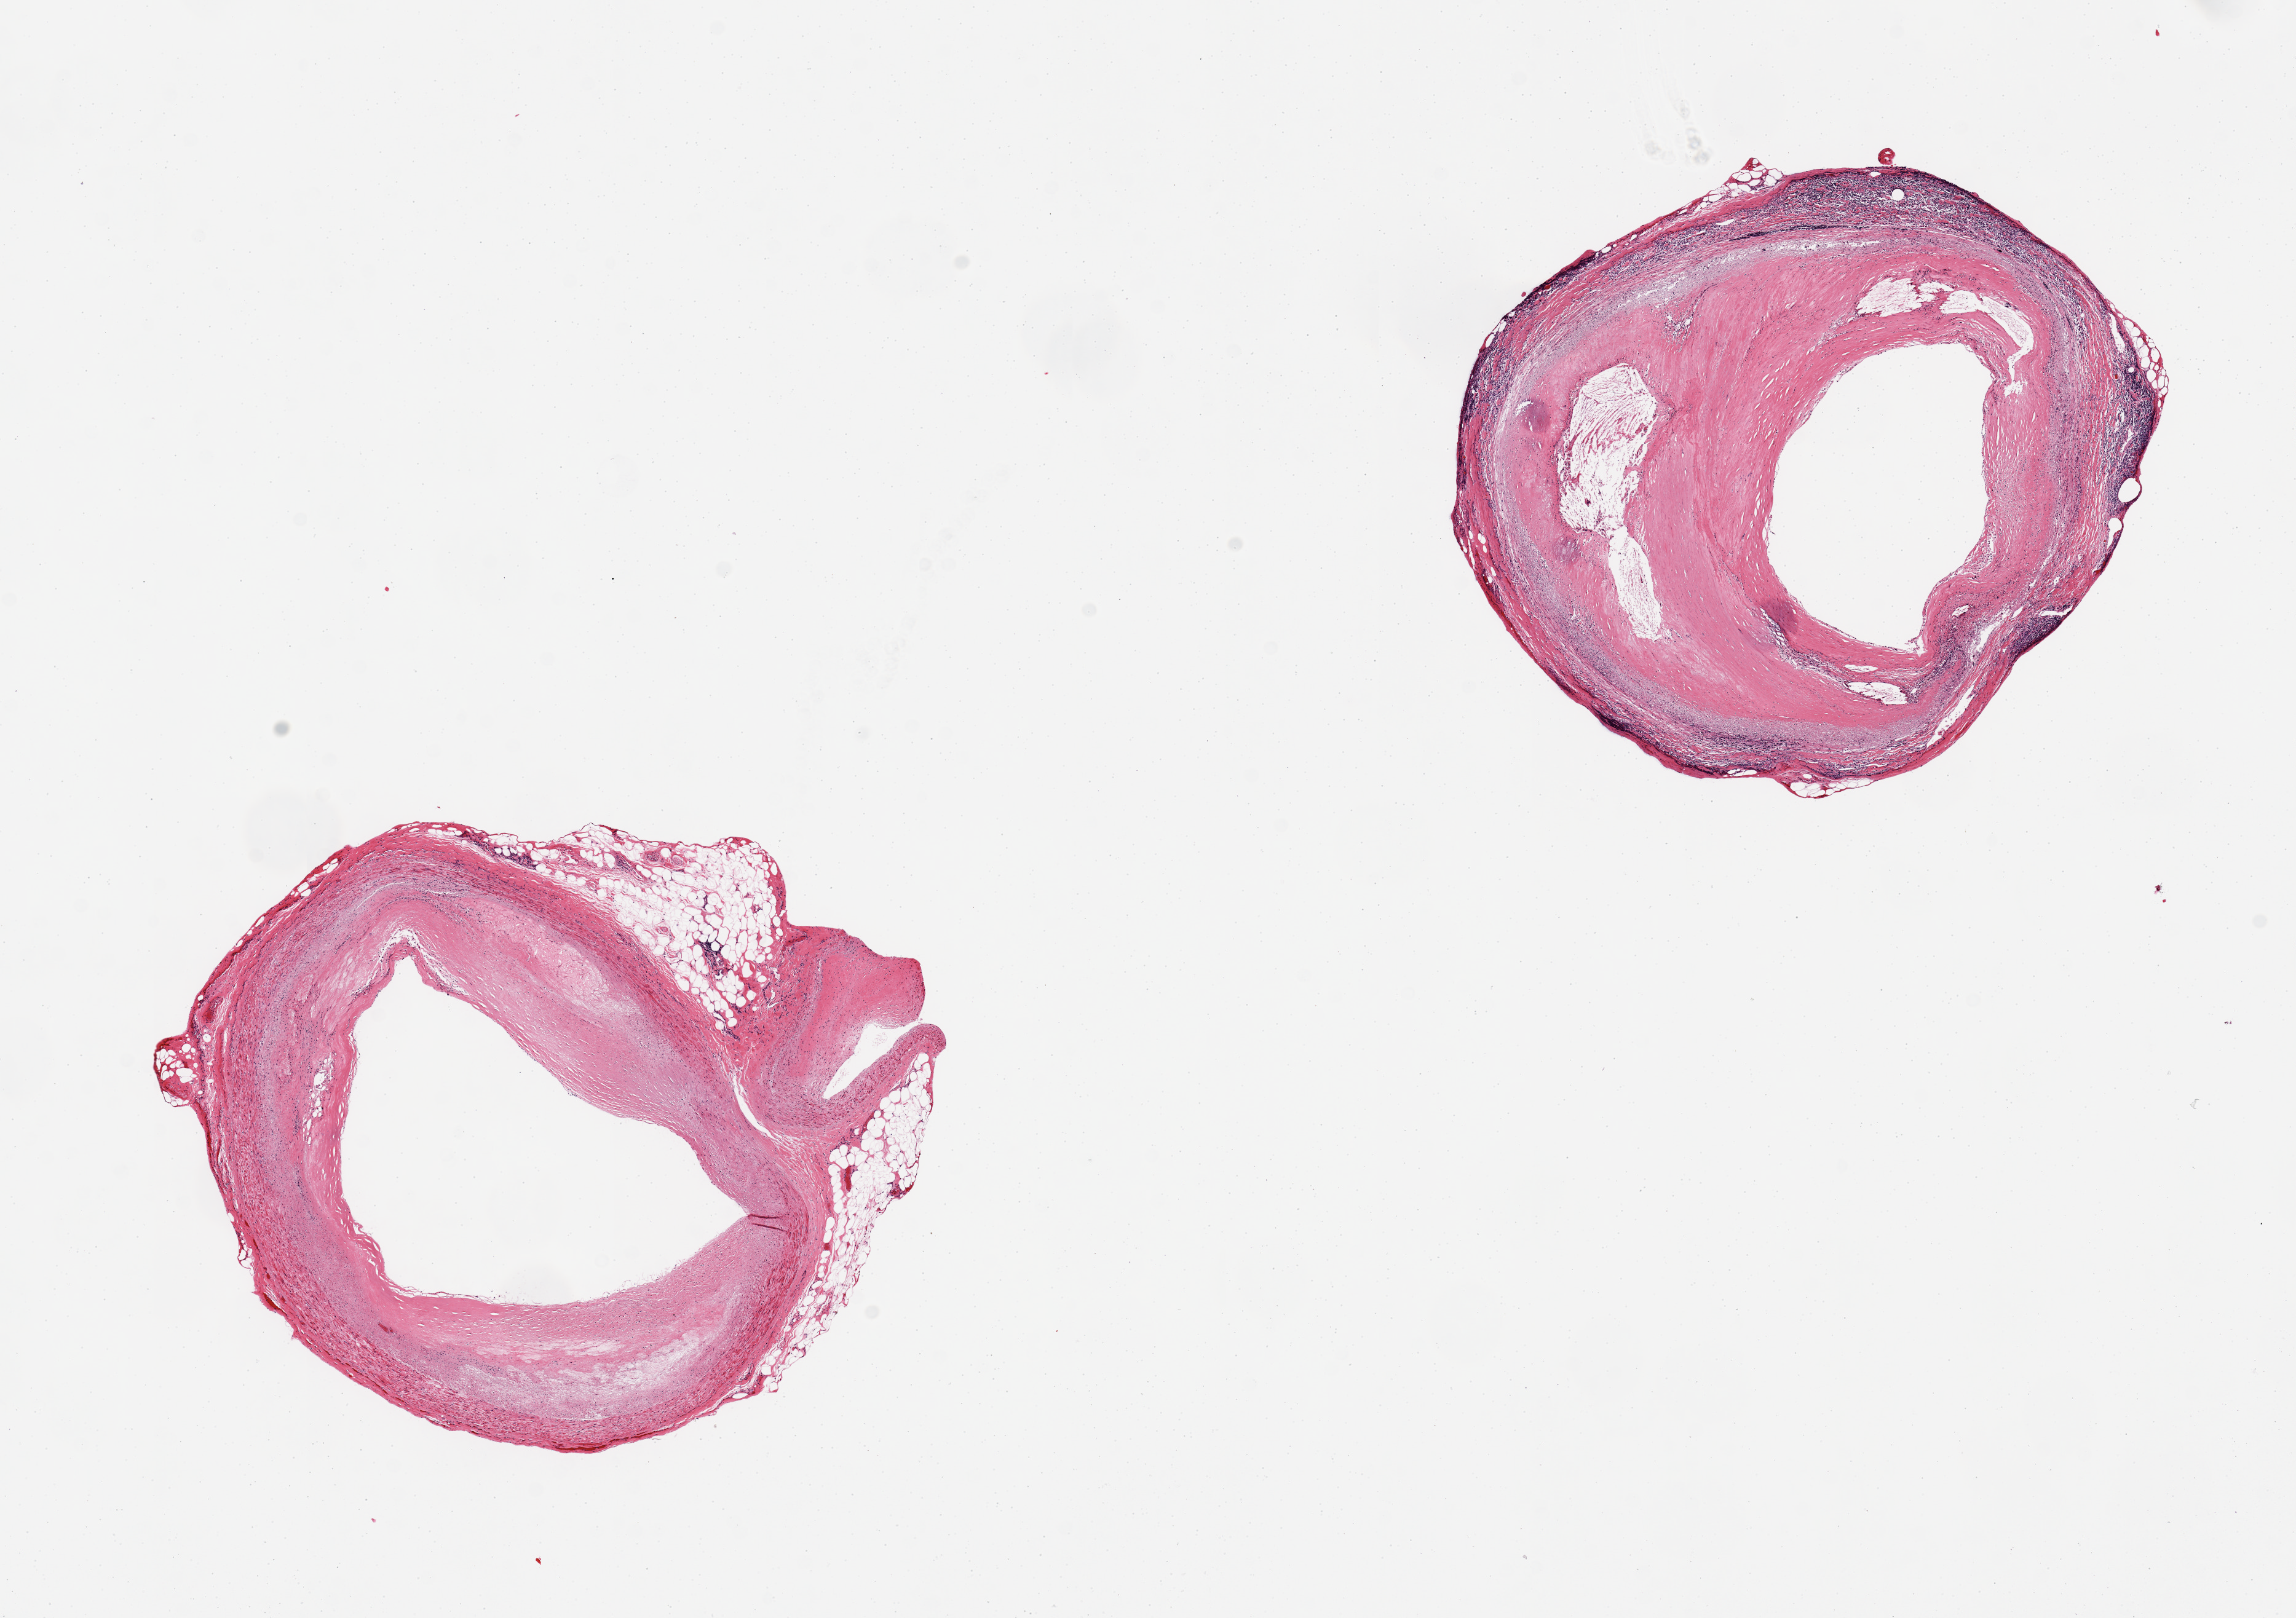
Digitized haematoxylin and eosin-stained section, low-resolution overview of the scanned area, about 14.8 x 10.4 mm. PAXgene-fixed, paraffin-embedded tissue. Section of coronary artery (target tissue). Tissue donor sample.
Review note (as recorded): 2 pieces, atherosclerosis with compromise of the lumen ~60%, peripheral cuff of inflammatory cells on 1 piece.